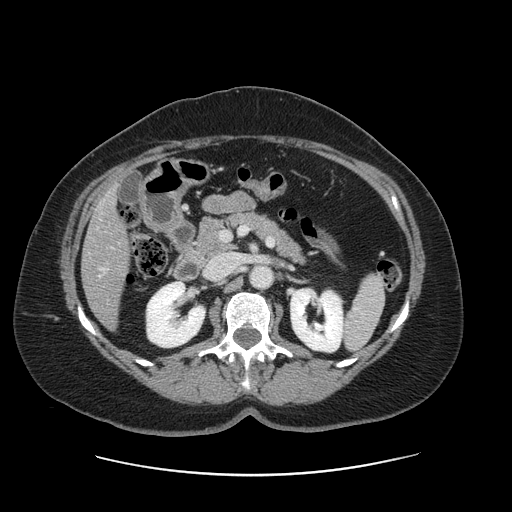
Contrast-enhanced abdominal CT, one axial slice. Slice 63 of 161 in the series (ordered by position). 120 kVp. Intravenous contrast given. Soft-tissue window (W 400 / L 40 HU). 2.5 mm slice thickness. 512 × 512 image matrix, field of view 398 × 398 mm. Female patient, age 62 years. From the clinical record (not read from this slice): diagnosis: colorectal cancer liver metastases, imaged before liver resection; multiple liver metastases: no; largest metastasis: 2.5 cm; disease in both lobes: no.
Structures marked on this image (expert manual segmentation):
- liver: bounding box <83,190,130,327> (left, top, right, bottom; pixels)